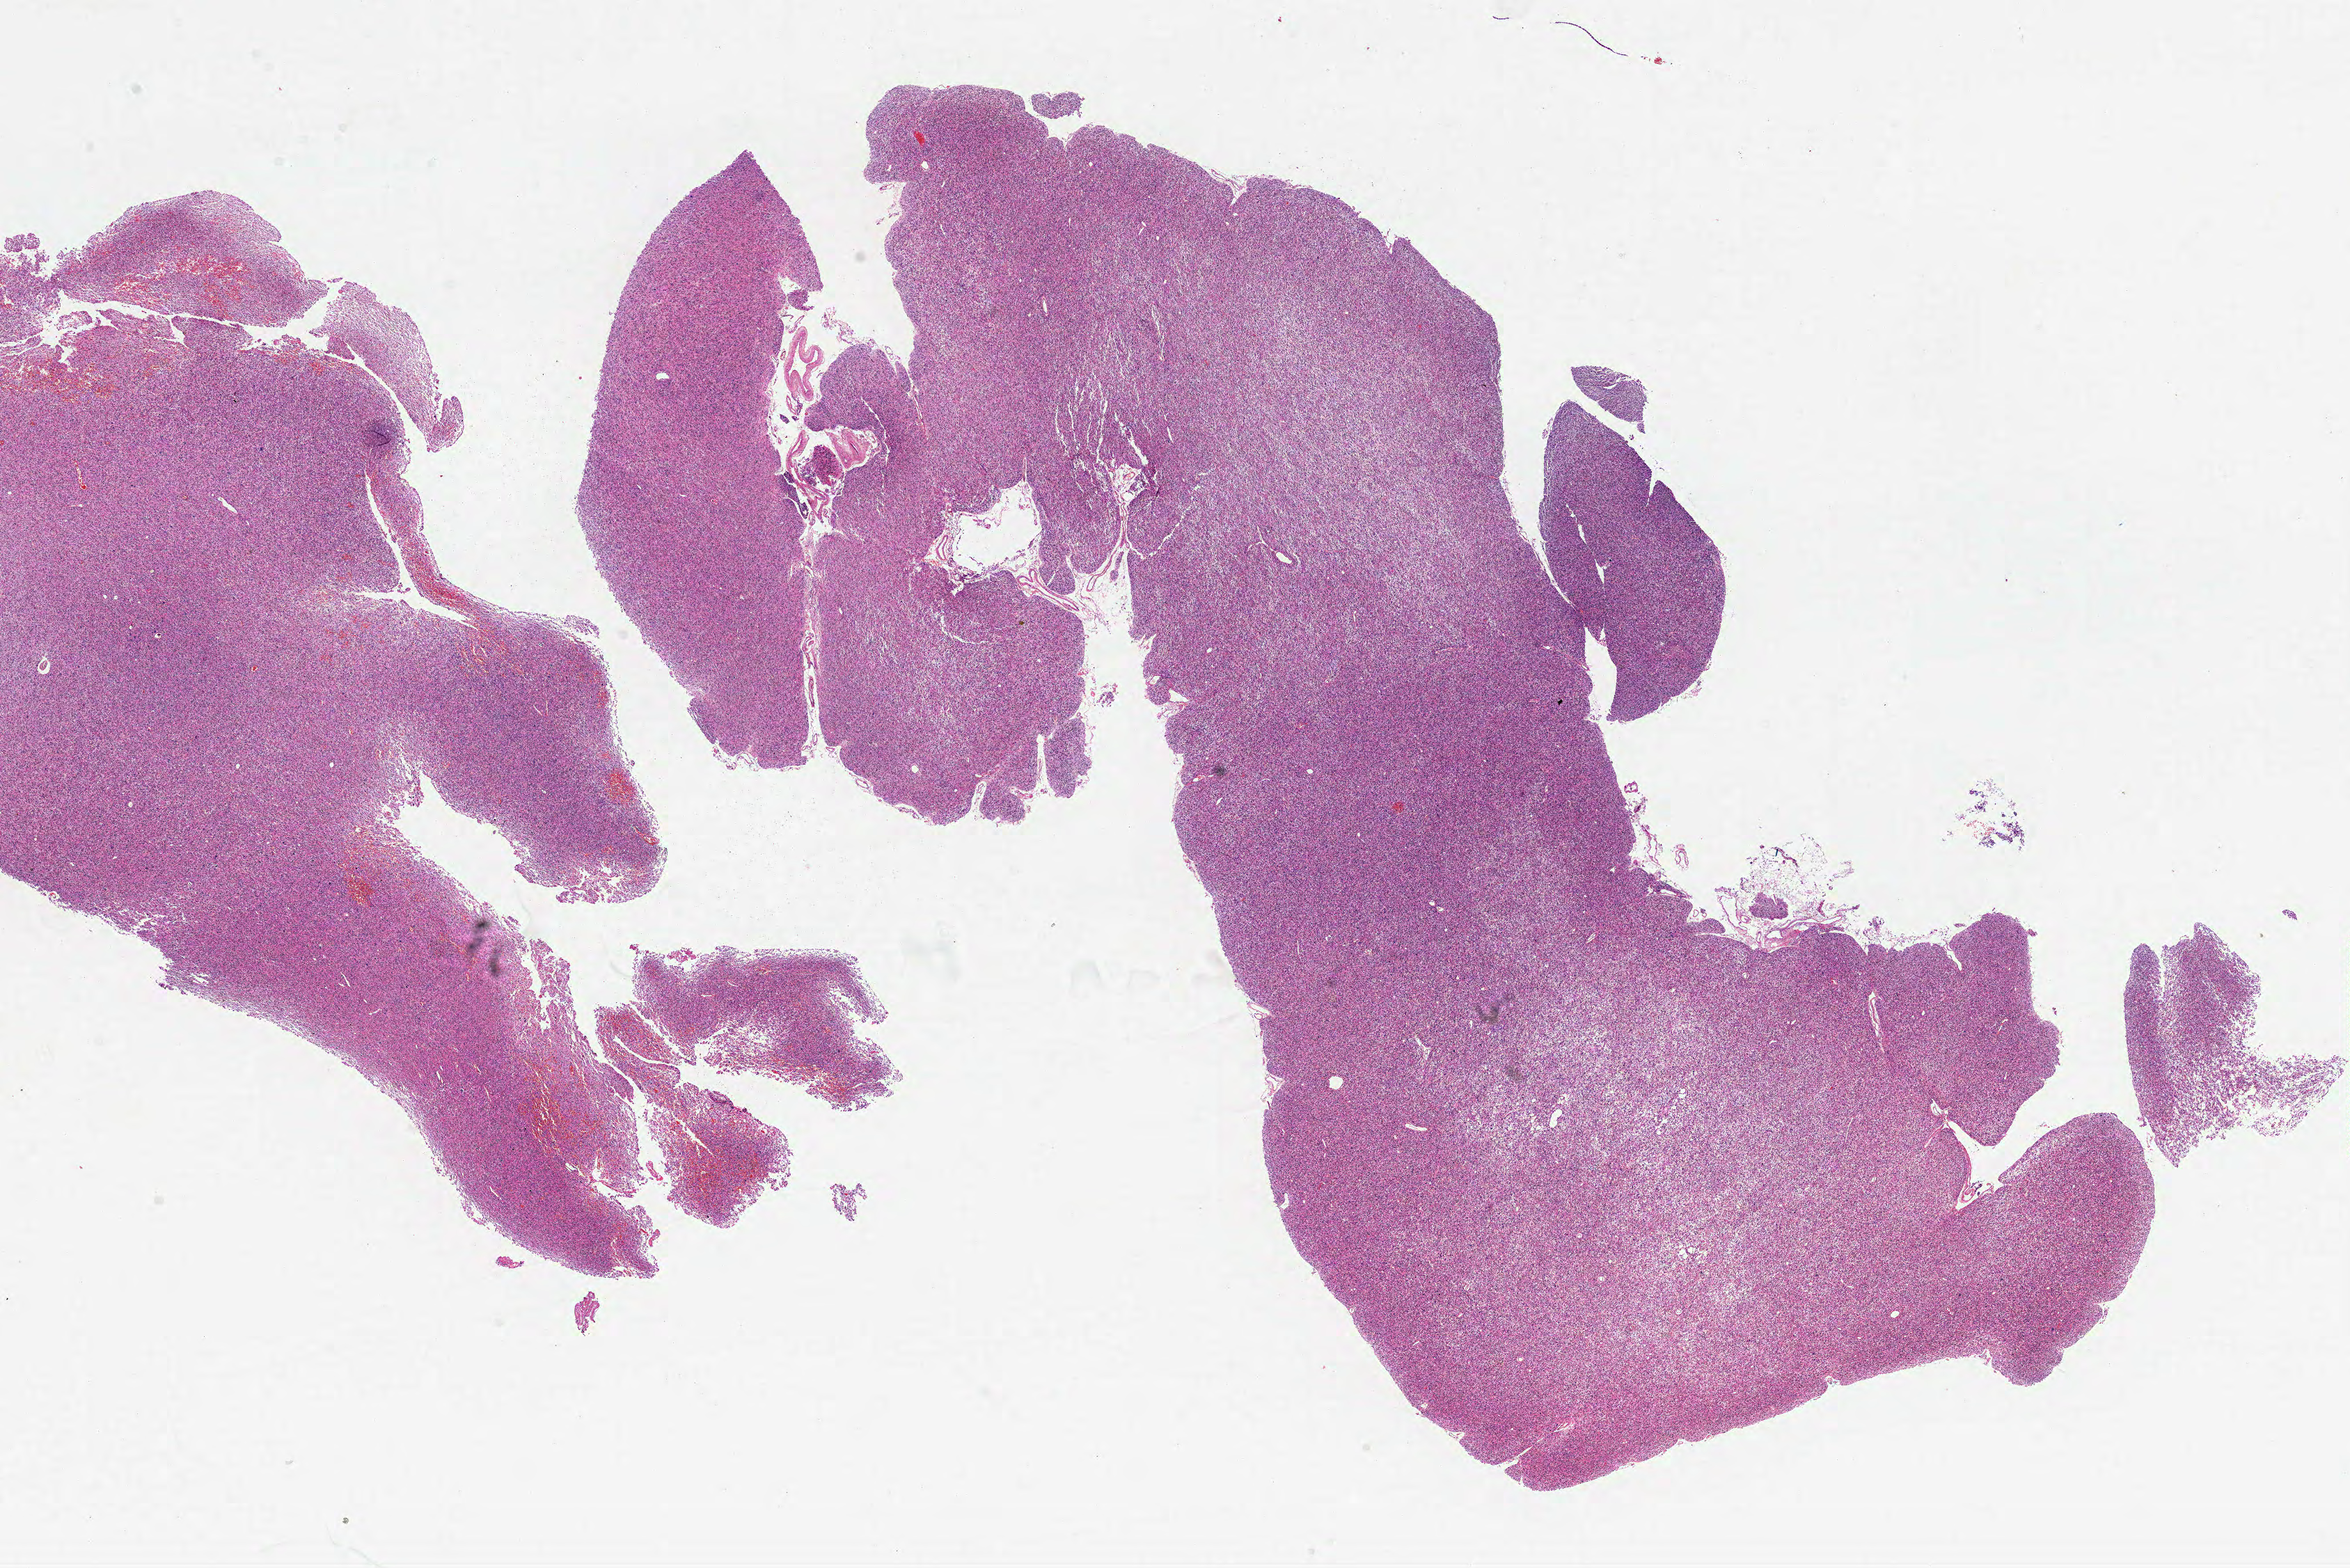
Digitized Hematoxylin and eosin (H&E) stained tissue section (whole slide) — whole scanned area (about 27.0 x 18.0 mm, slide scanned at 20x) shown as a low-resolution overview; FFPE section; sample: primary tumour, brain. Patient: male, age at initial diagnosis 63 years.
Pathologic diagnosis: Glioblastoma.